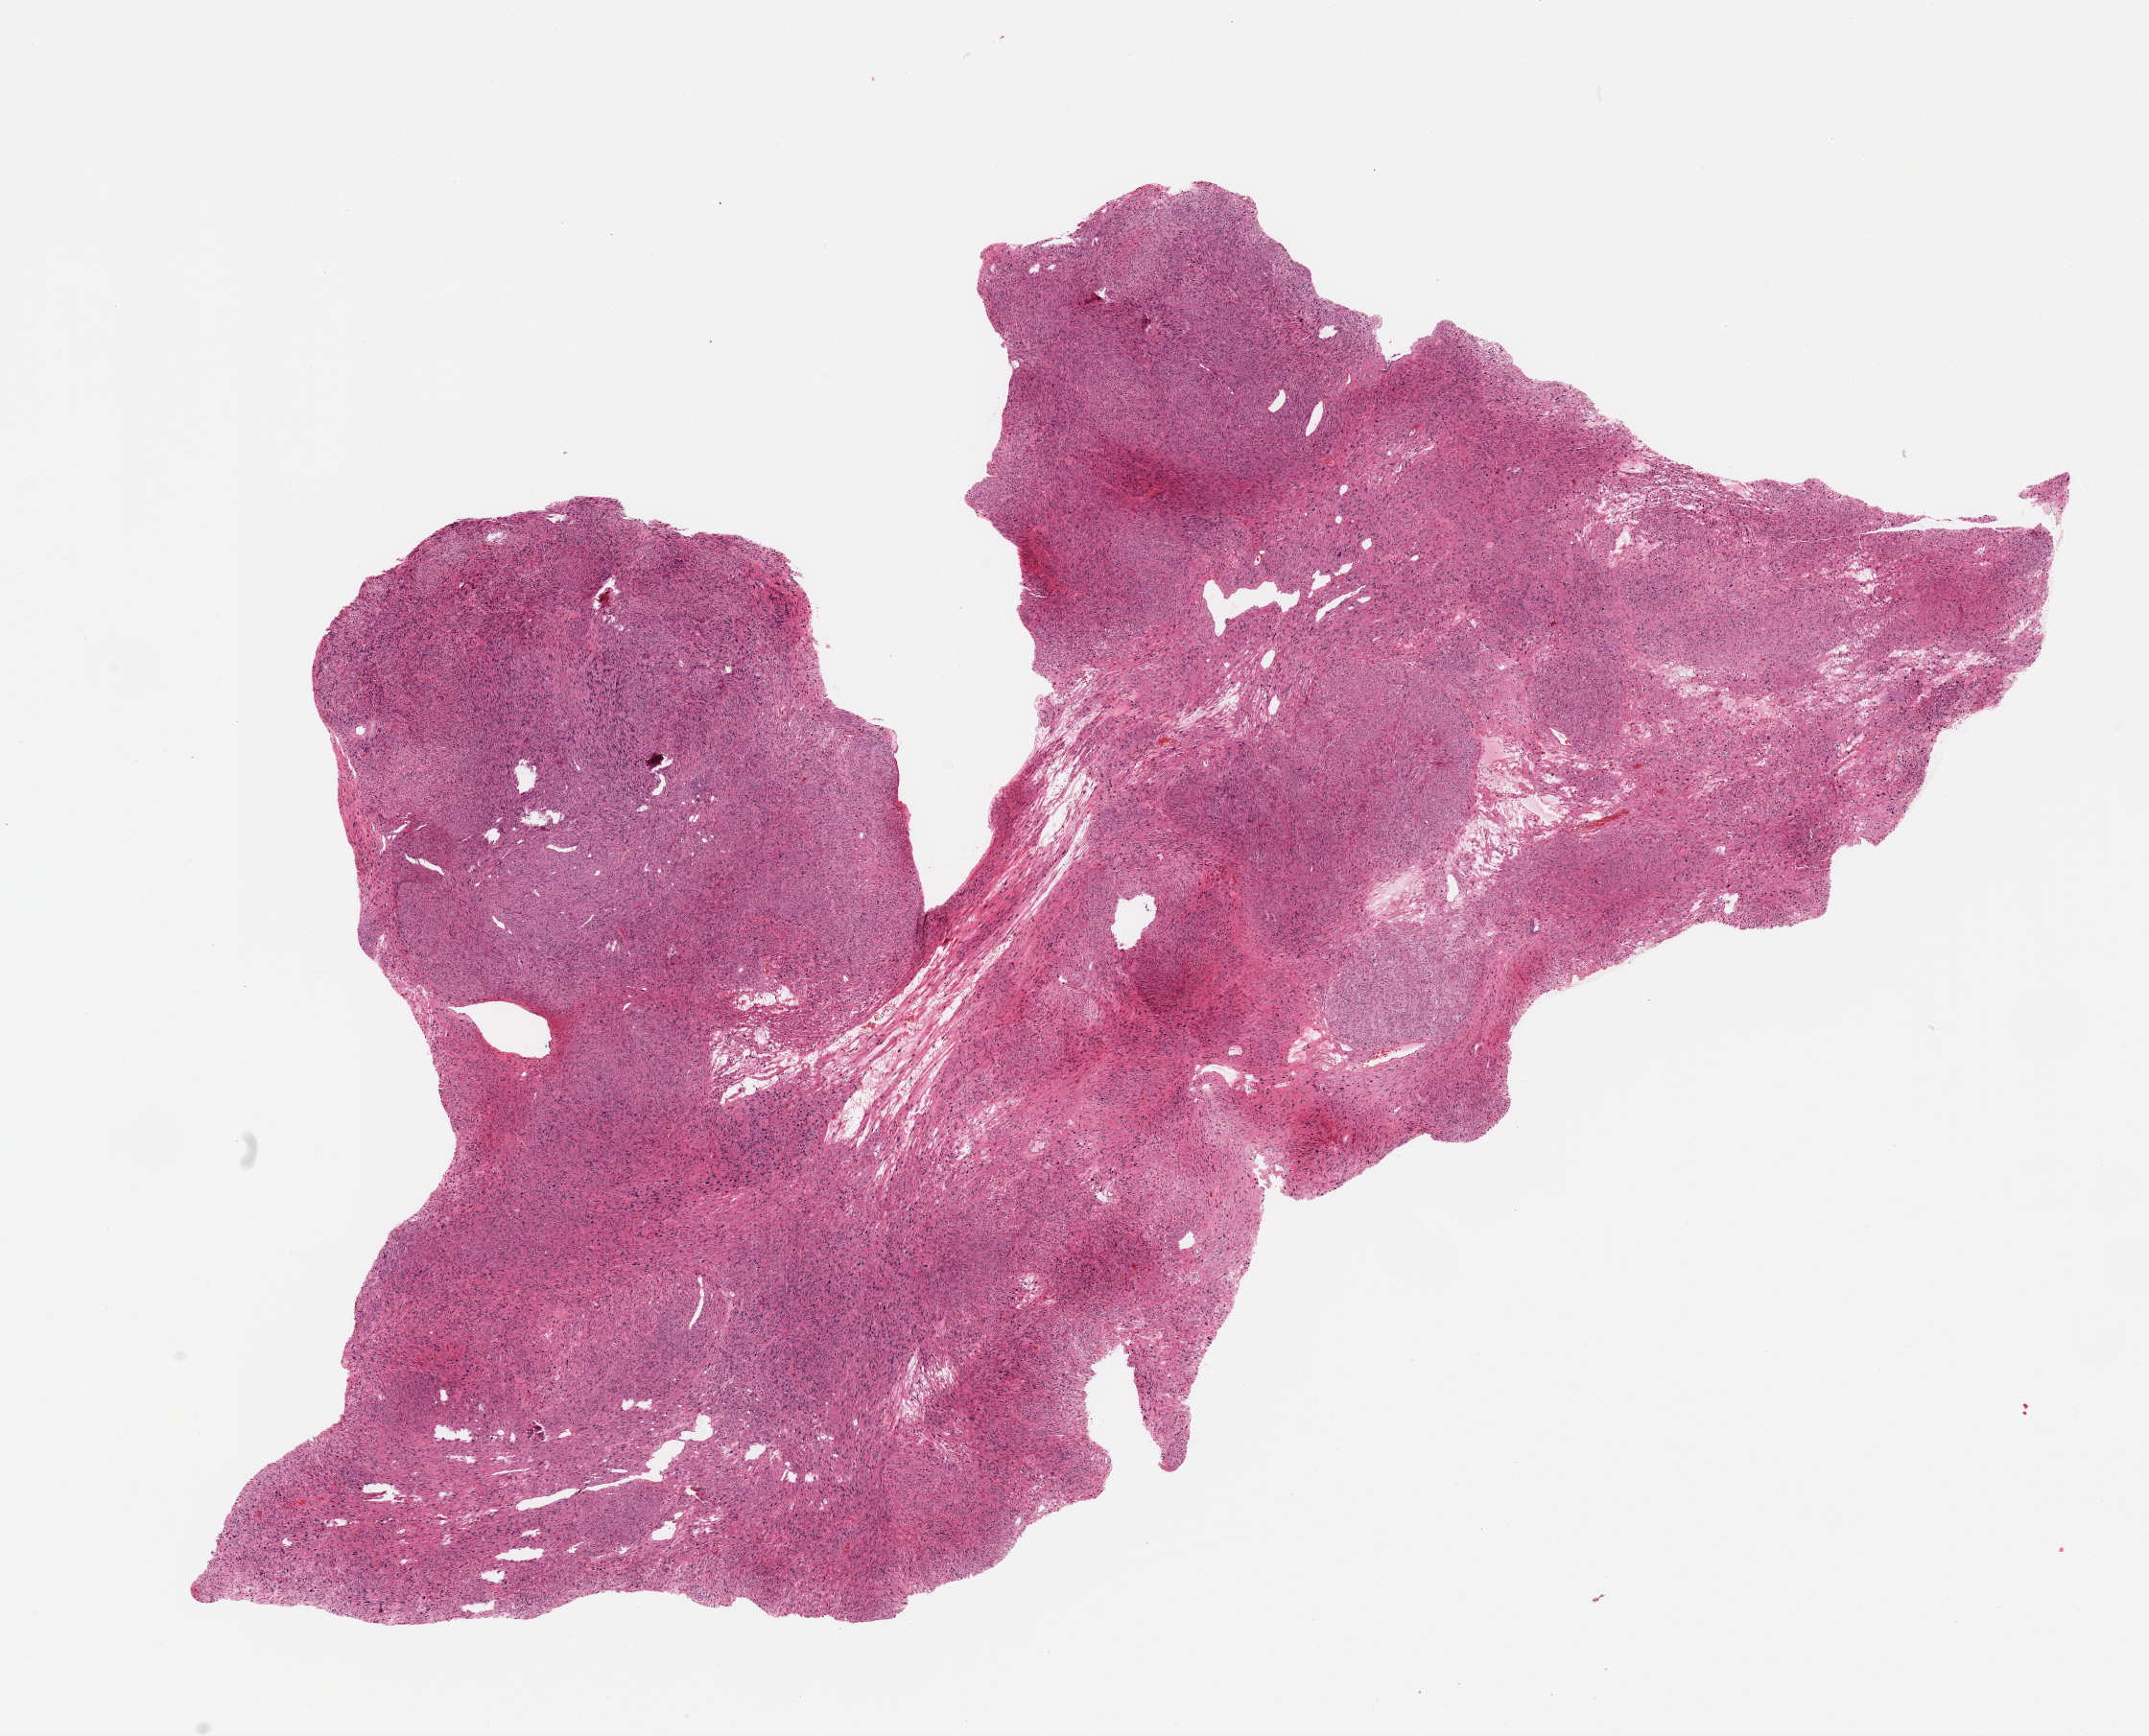
Whole-slide histology image, H&E — whole scanned area (about 17.7 x 14.3 mm, from a 20x scan) shown as a low-resolution overview, tumour tissue sample. Patient: male, age 53 years.
* patient diagnosis (cohort enrolment): sarcoma (site not recorded at cohort level)
* primary tumour site (as recorded): retroperitoneum